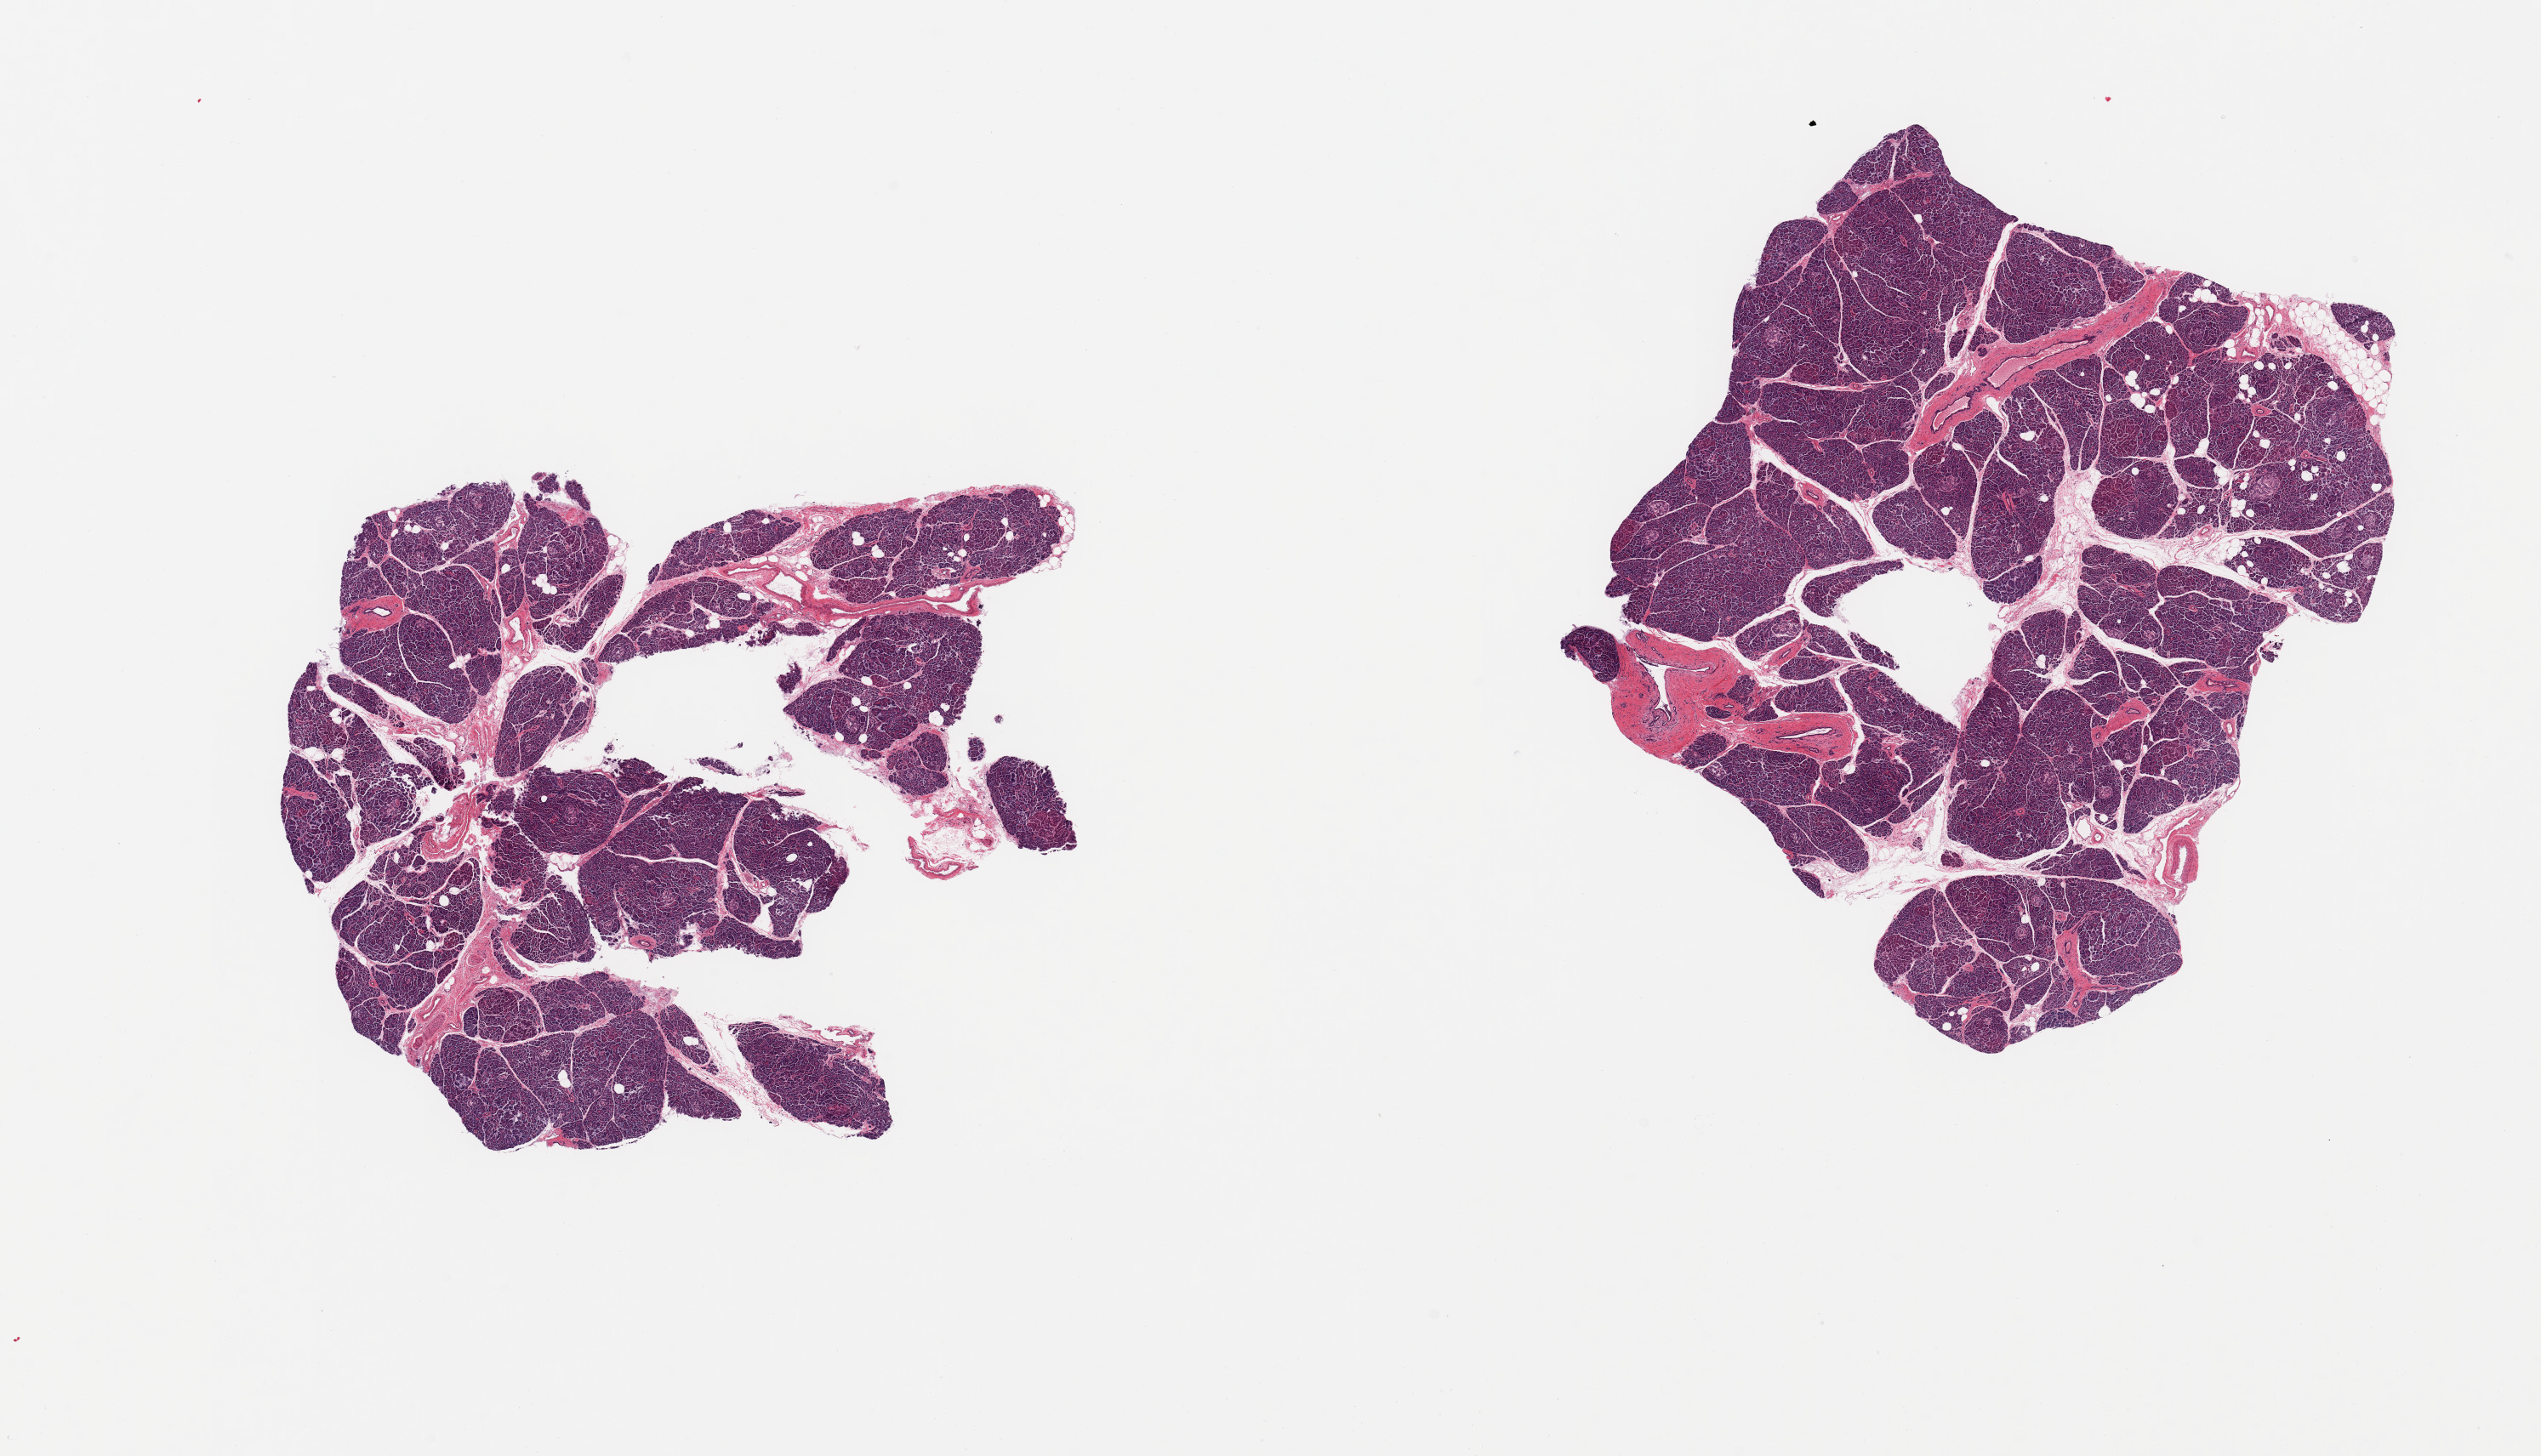
Whole-slide image, hematoxylin and eosin (H&E) stain, brightfield — whole scanned area (about 23.6 x 13.5 mm, acquisition: 20x scan) shown as a low-resolution overview. PAXgene-fixed, paraffin-embedded tissue. Section of pancreas (target tissue). Donor tissue sample. Male donor.
• reviewer comment on this tissue sample: 2 pieces